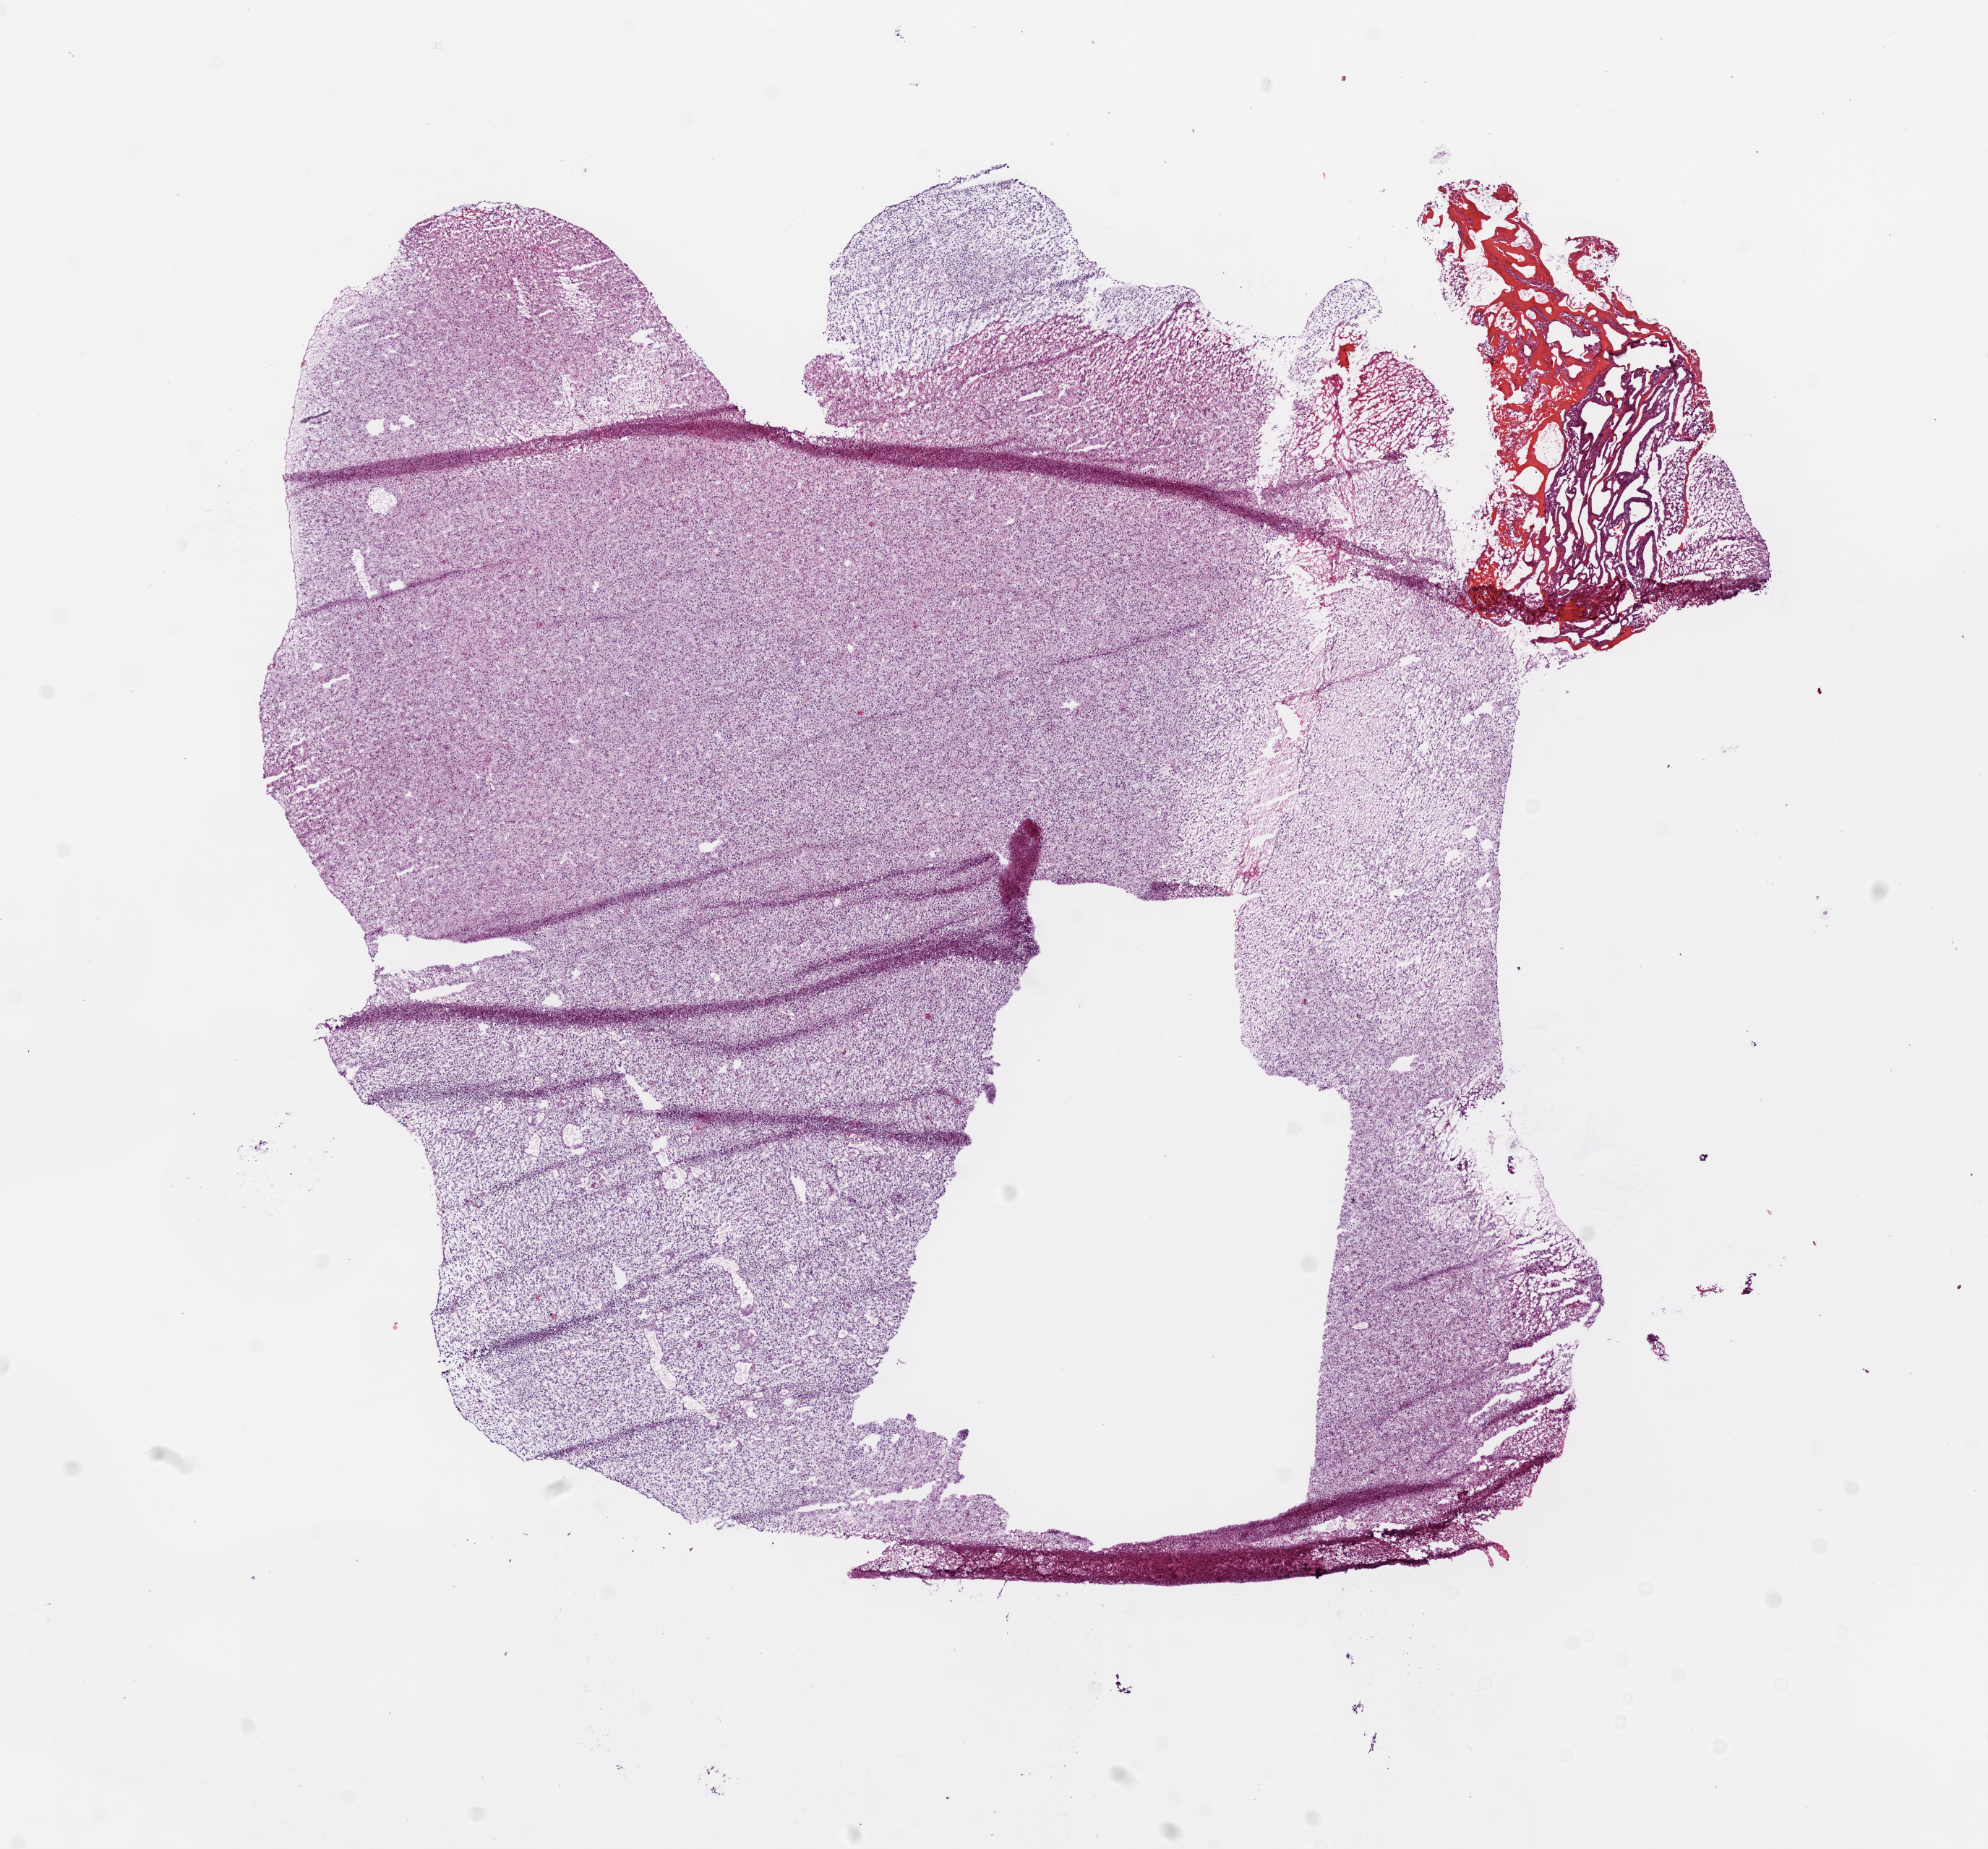
Whole-slide histology image, H&E-stained, low-resolution overview of the scanned area, about 11.0 x 10.3 mm (slide scanned at 20x). Frozen section. Primary tumour sample from the brain. Patient: male, age at initial diagnosis 46 years. Slide review estimates, as recorded: tumour cells 85%, tumour nuclei 85%, normal cells 0%, stromal cells 5%, necrosis 10%.
• histologic diagnosis: Glioblastoma